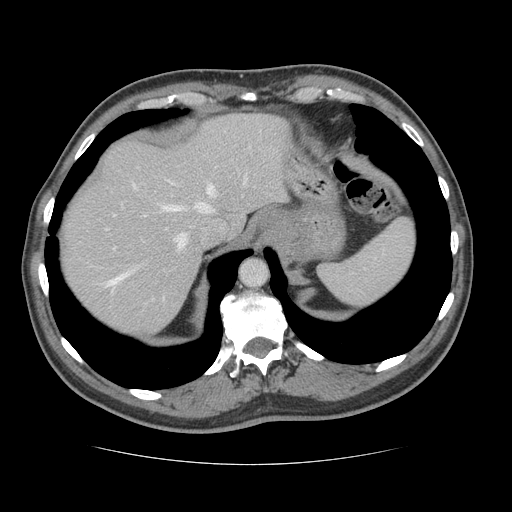
Contrast-enhanced abdominal CT, one axial slice; position 106 of 134 along the scan axis; 120 kVp; soft-tissue window (W 400 / L 40 HU); 2.5 mm slice thickness; 512 × 512 image matrix, field of view 377 × 377 mm. Male patient, age 68 years. From the clinical record (not read from this slice): diagnosis: colorectal cancer liver metastases, imaged before liver resection; multiple liver metastases: yes; largest metastasis: 2.2 cm; chemotherapy before resection: no.
Outlined on this slice (manually delineated by an expert):
- hepatic veins: bounding box <106,174,247,285> (left, top, right, bottom; pixels)
- liver: <61,113,286,335>
- planned liver remnant (the part of the liver to remain after resection): <61,114,287,317>